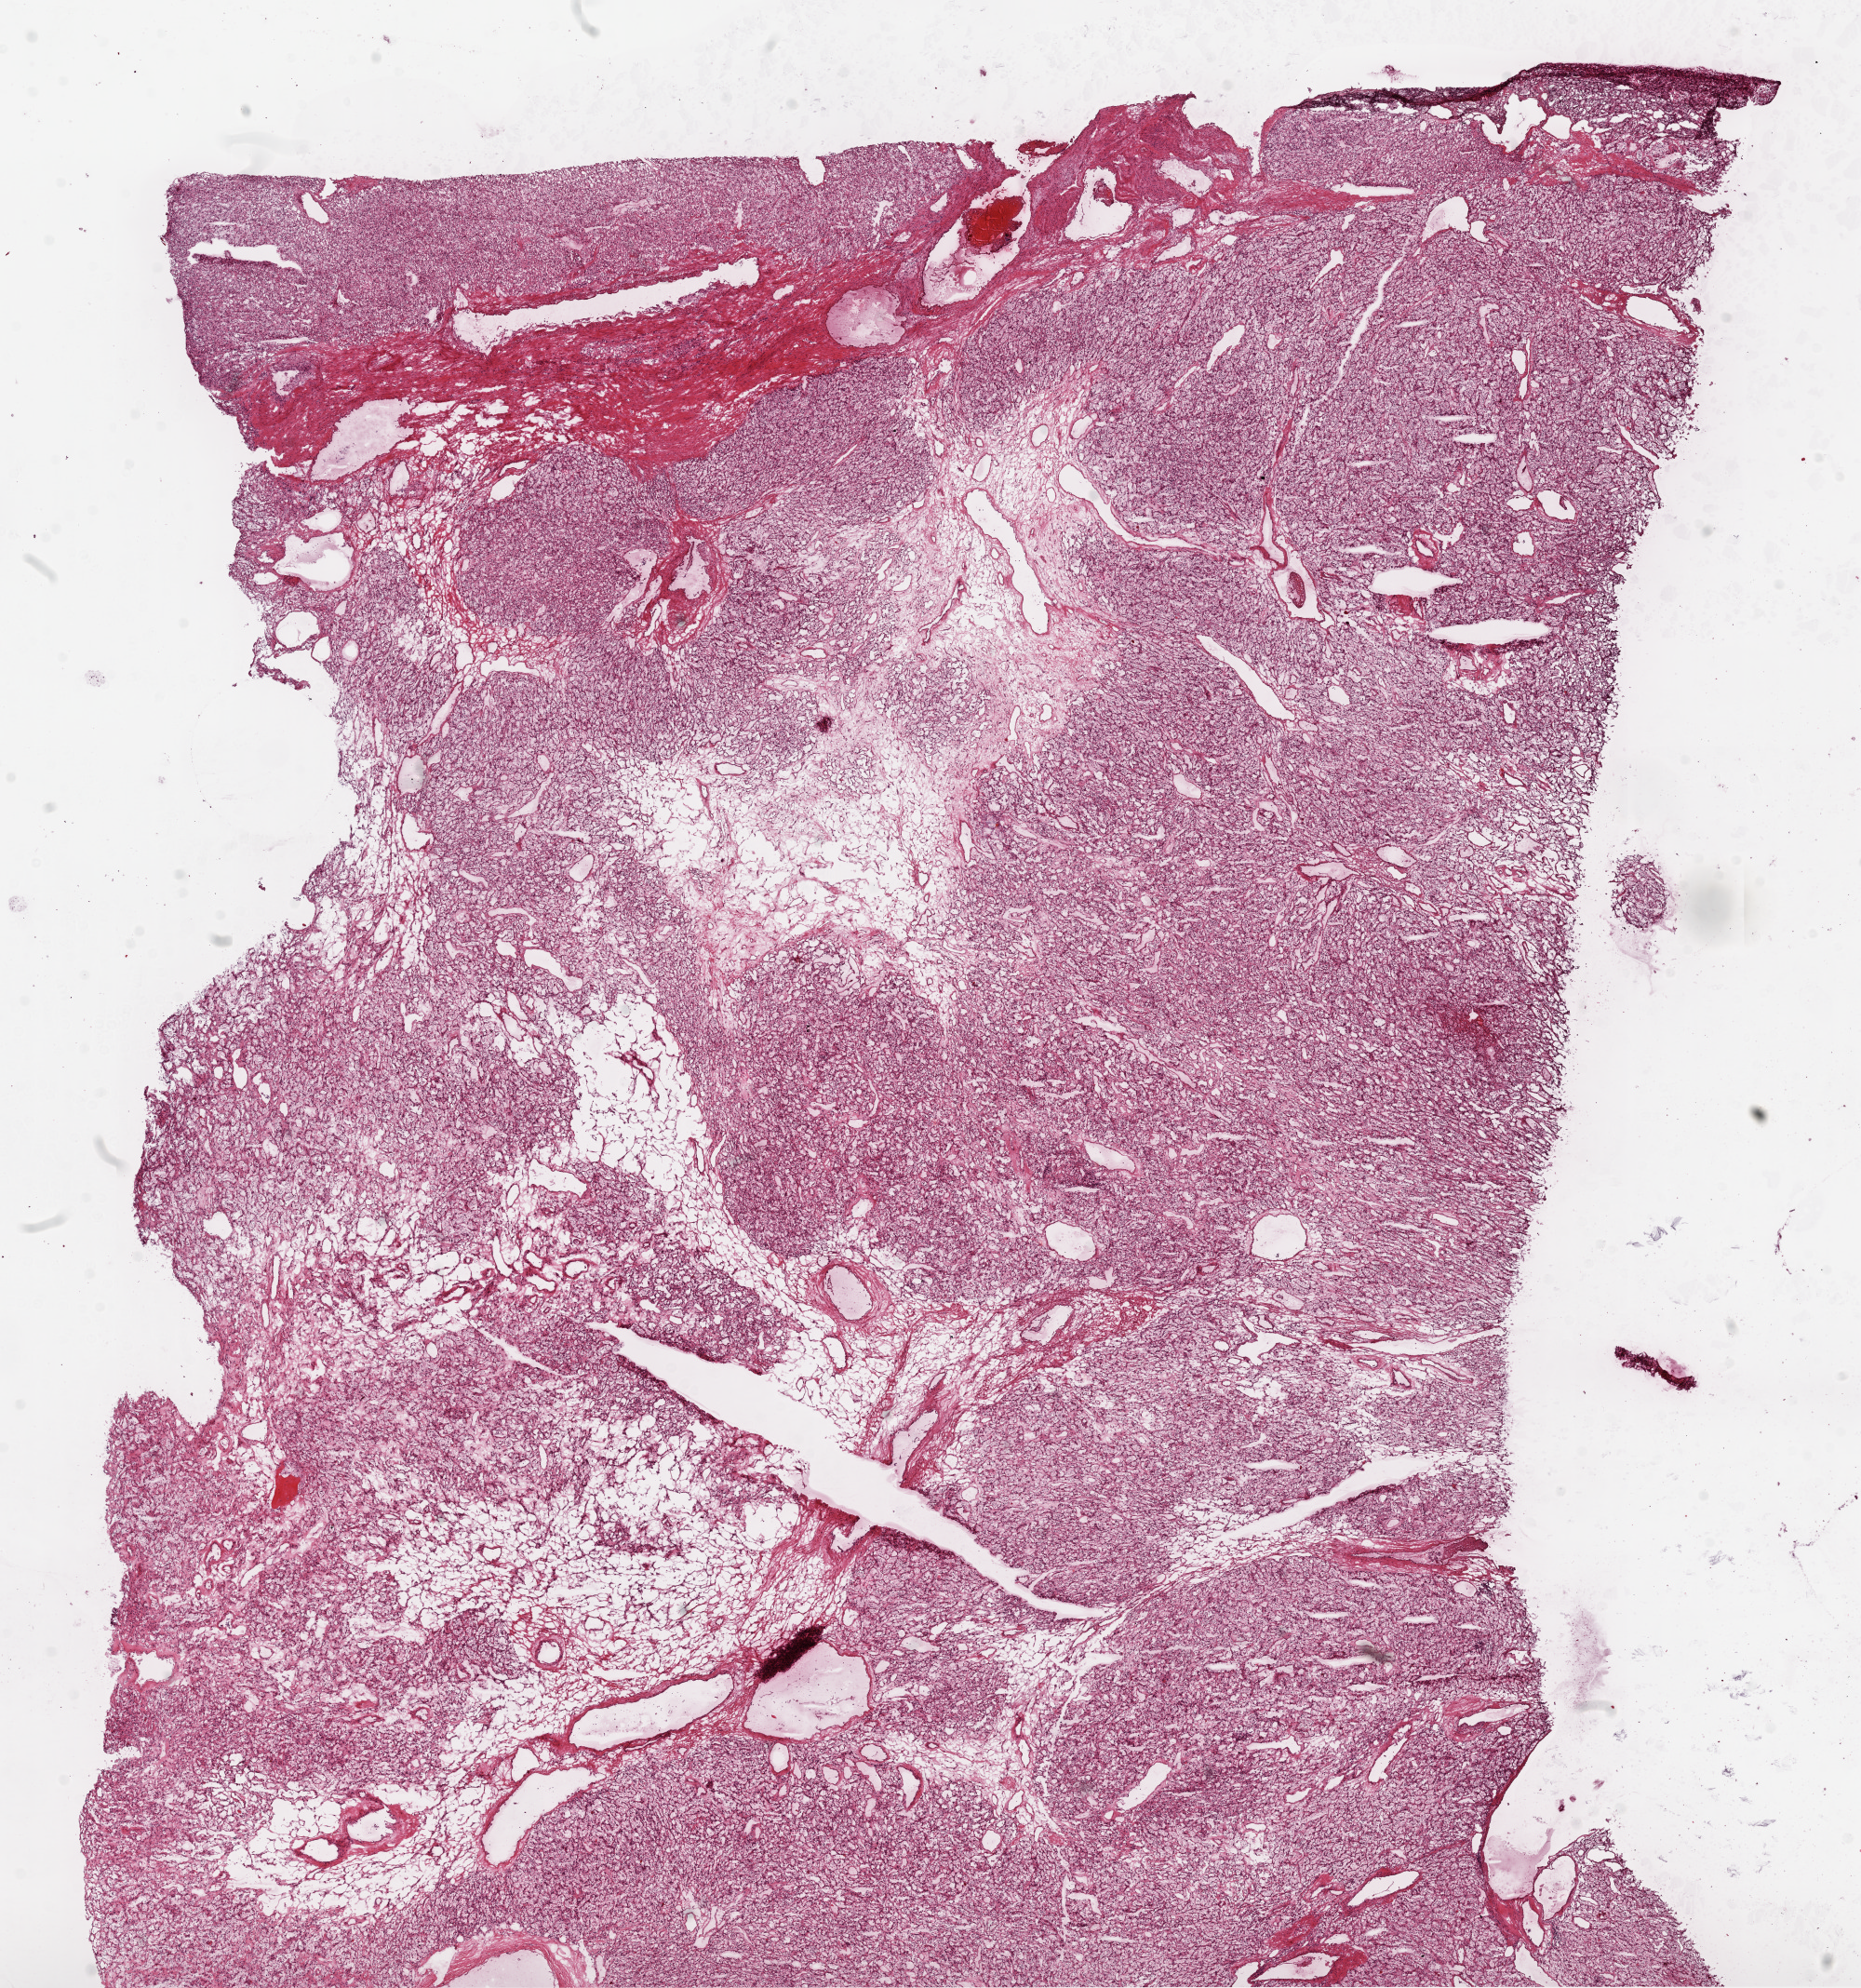
Whole-slide histology image, H&E — whole scanned area (about 16.0 x 17.1 mm) shown as a low-resolution overview; frozen section from the top of the tissue portion; sample: primary tumour, kidney. Female patient; age at initial diagnosis 59 years.
Histologic diagnosis: Clear cell adenocarcinoma, NOS.